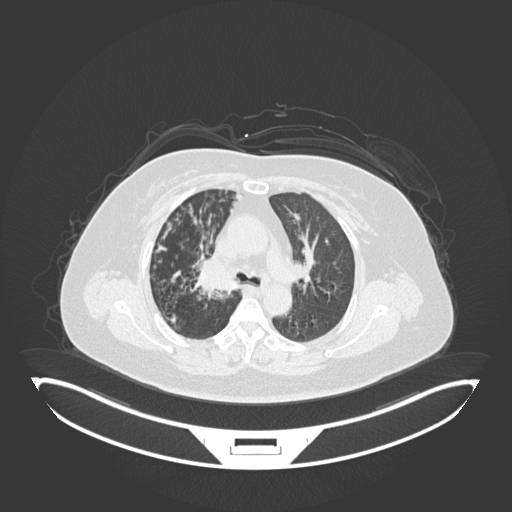
Chest CT, one axial slice; position 118 of 245 along the scan axis; 120 kVp; lung window (W 1500 / L -600 HU); 1 mm slice thickness; 512 × 512 image matrix, field of view 500 × 500 mm. Female patient, age 60 years. From the clinical record (not read from this slice): clinical TNM (as recorded): T1c N0 M0; histopathological grade: G1-G2.
Annotated regions visible in this slice (rectangle marked by the reading radiologist):
- lung tumour (recorded histology: squamous cell carcinoma): bounding box [x1, y1, x2, y2] px = [192, 252, 245, 294]